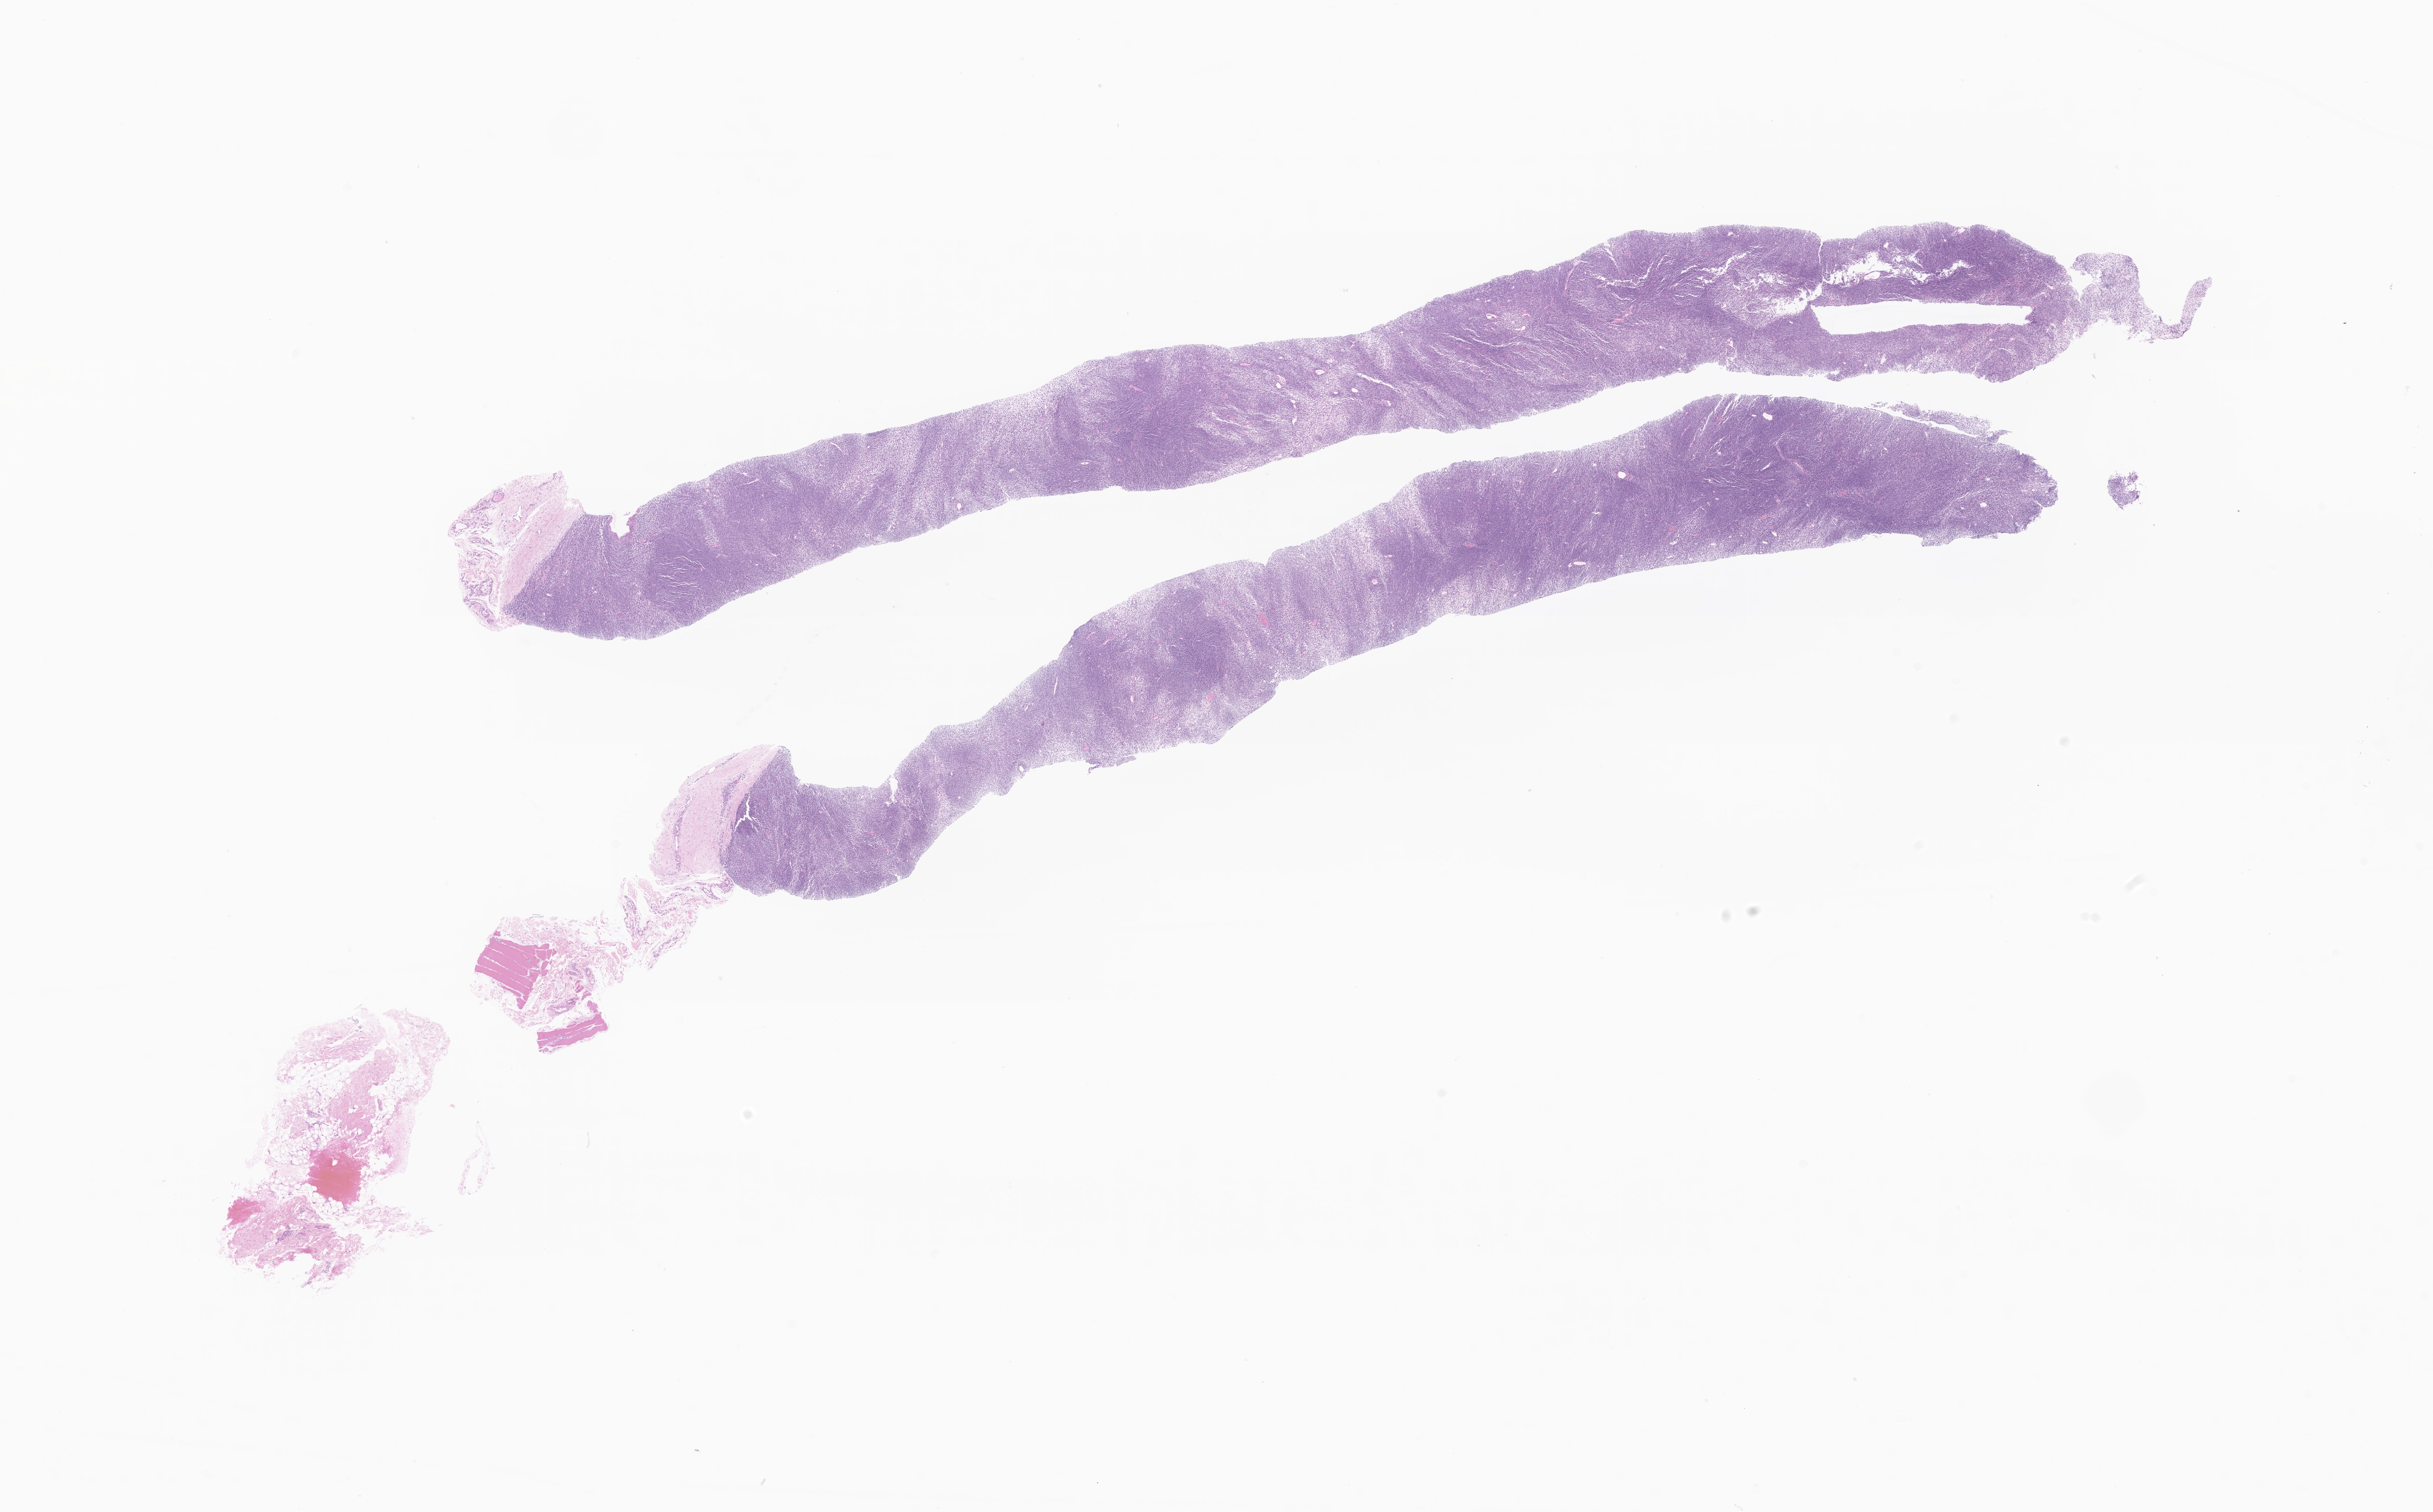
H&E whole-slide image of tumor tissue from the soft tissue of lower extremity — whole scanned area (about 20.3 x 12.6 mm) shown as a low-resolution overview, formalin-fixed, paraffin-embedded (FFPE) tissue. Male patient, age 229 months (19 years 1 month).
* recorded diagnosis: Synovial sarcoma, NOS